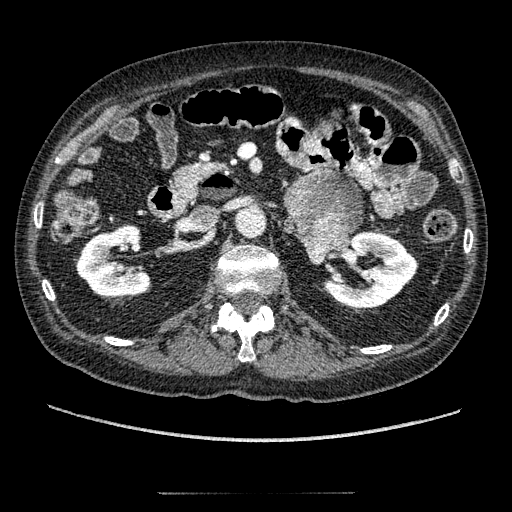
Contrast-enhanced abdominal CT, one axial slice. Slice 98 of 274 in the series (ordered by position). Reconstruction kernel STANDARD. 120 kVp. Soft-tissue window (W 400 / L 40 HU). 1.25 mm slice thickness. 512 × 512 image matrix. Patient: male, 69 years. Case-level facts recorded for this patient, not image findings: diagnosis: adrenocortical carcinoma; tumour side: left adrenal.
Structures marked on this image (semi-automatically segmented with operator editing):
- mass: box from (x=285, y=173) to (x=361, y=264) px